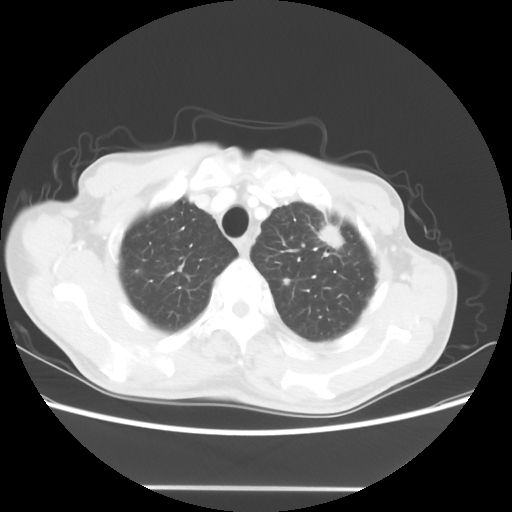
Chest CT, one axial slice. Slice 50 of 60 in the series (ordered by position). Reconstruction kernel STANDARD. Lung window (W 1500 / L -600 HU). 5 mm slice thickness. 512 × 512 image matrix, field of view 367 × 367 mm. Male patient, age 74 years. Case-level facts recorded for this patient, not image findings: clinical TNM (as recorded): T1c N0 M1a.
Annotated regions visible in this slice (rectangle marked by the reading radiologist):
- lung tumour (recorded histology: adenocarcinoma): bounding box (x1, y1, x2, y2) in pixels: (321, 225, 343, 246)